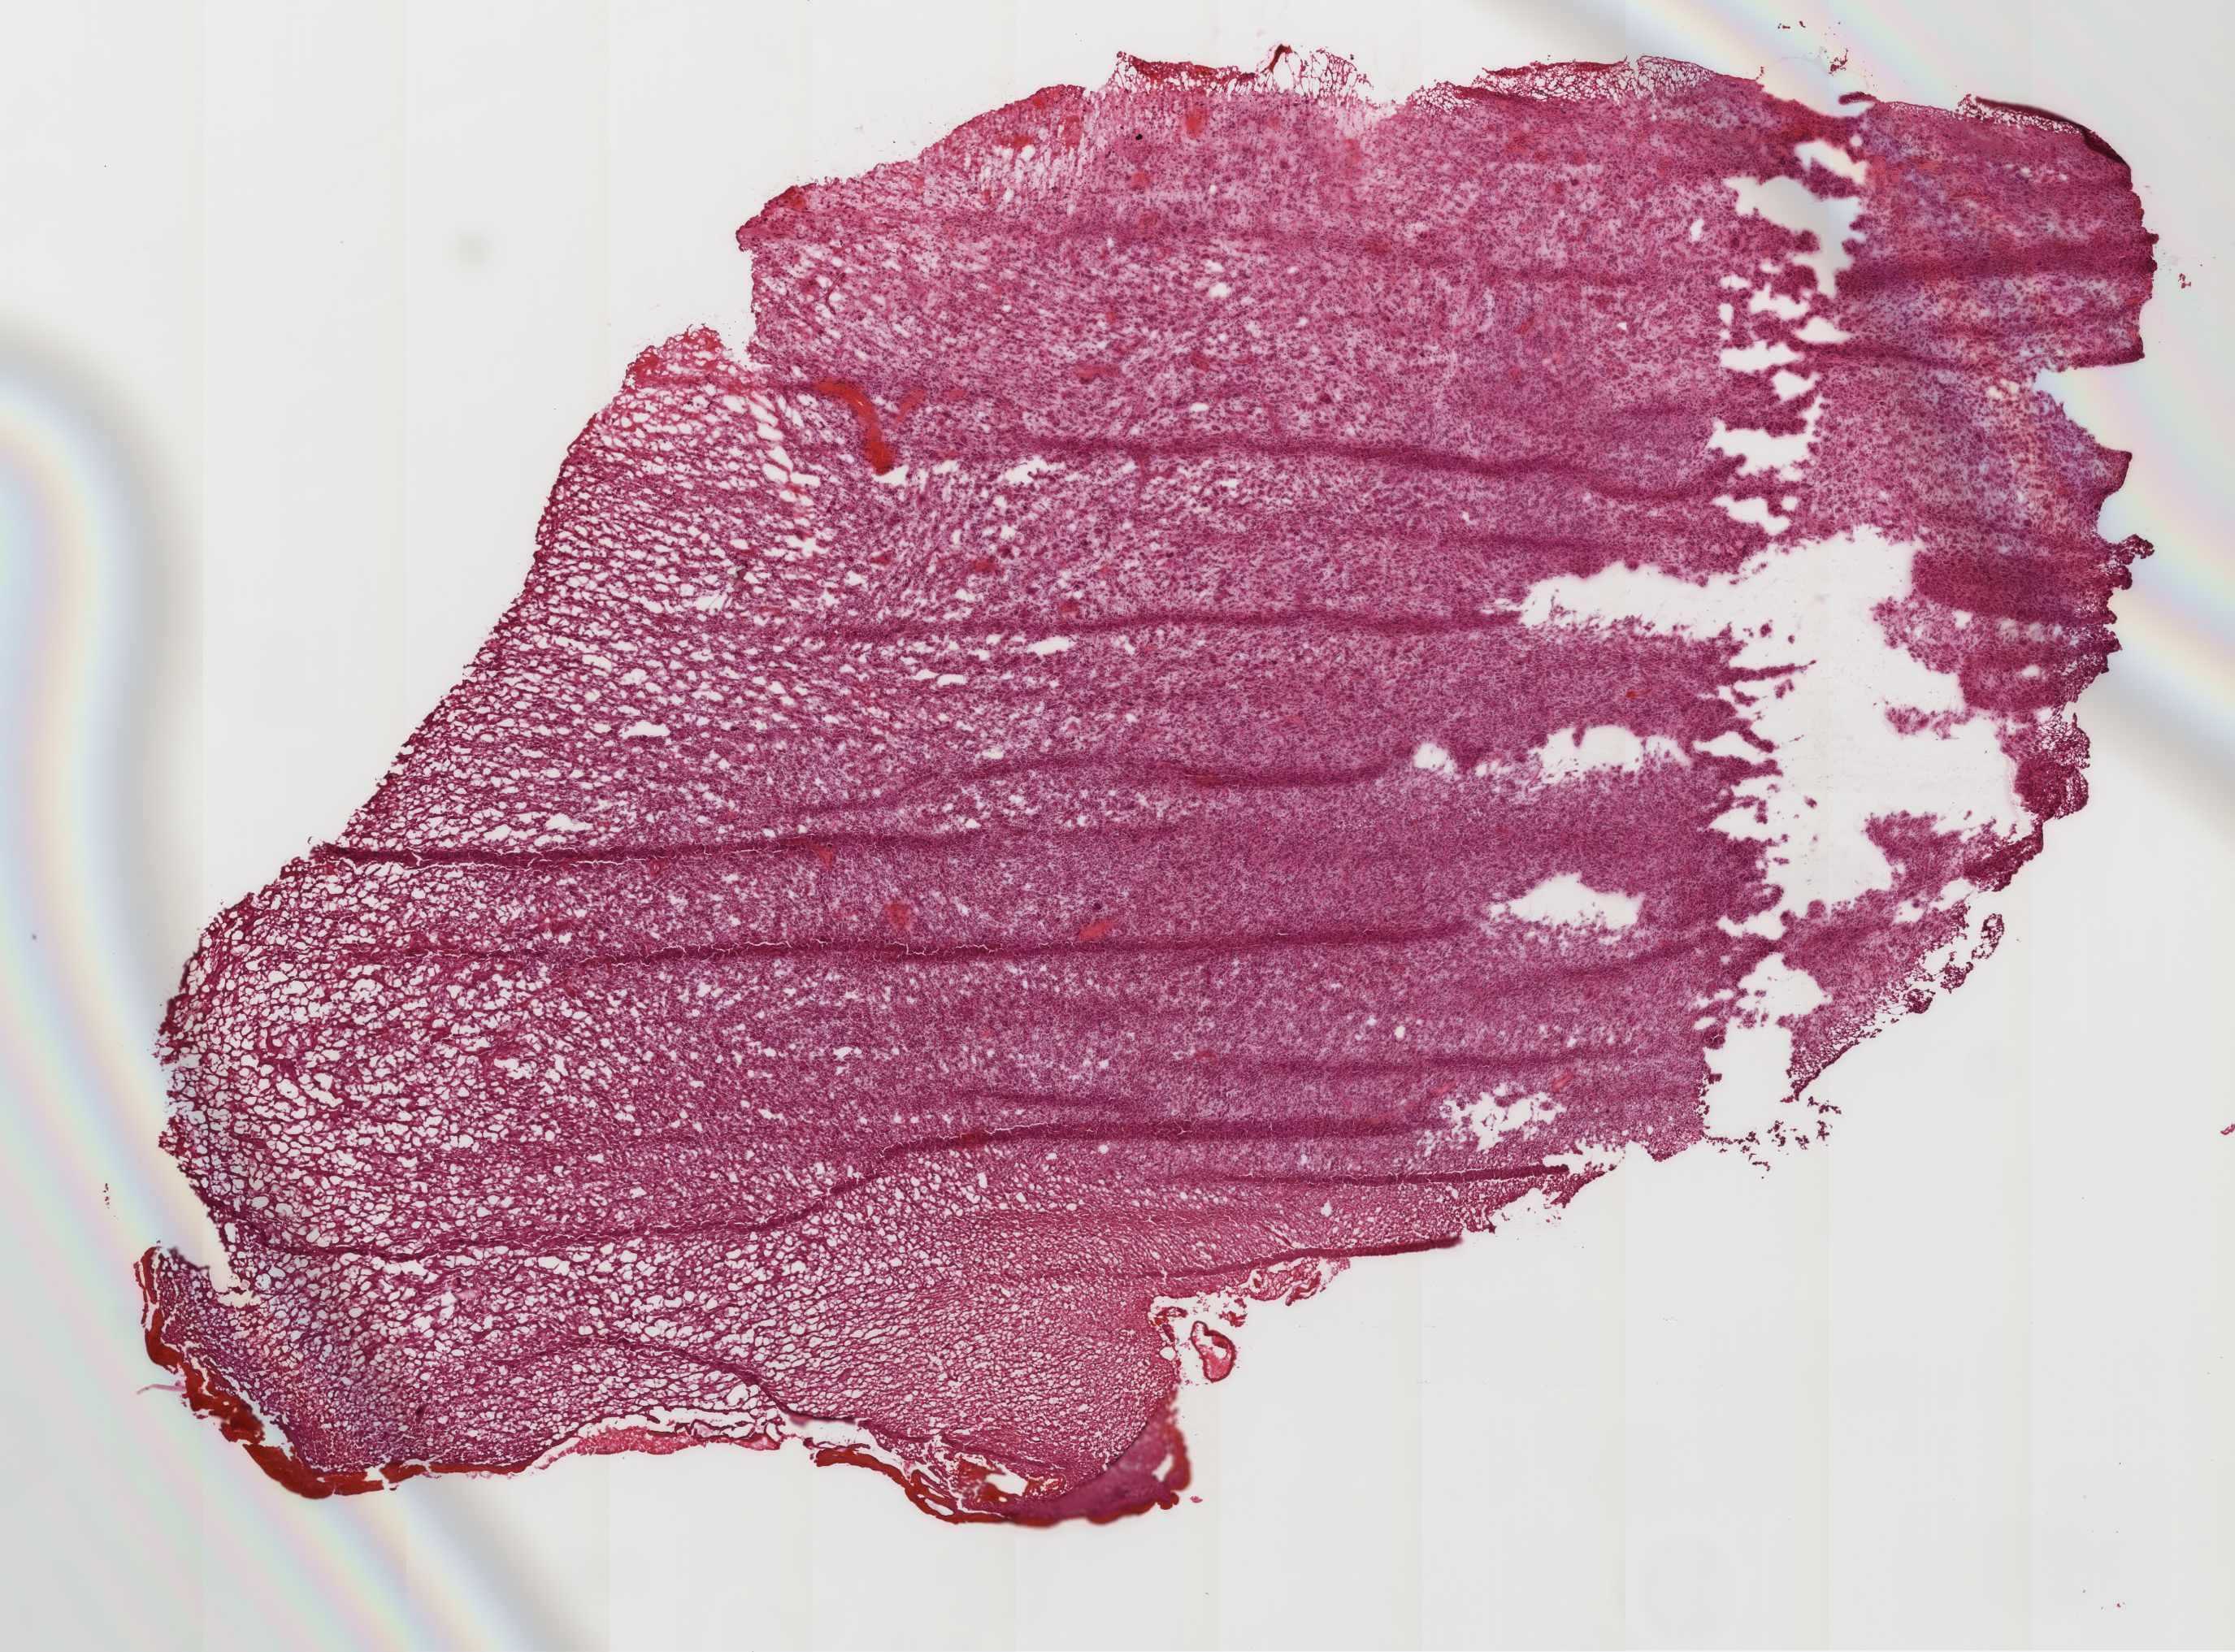
Whole-slide histology image, H&E-stained — a low-resolution overview of the entire scanned area, about 11.0 x 8.2 mm (slide scanned at 20x); frozen section from the top of the tissue portion; sample: primary tumour, brain. Female patient; age at initial diagnosis 59 years. Composition of this section per pathologist review: tumour cells 100%, tumour nuclei 85%, normal cells 0%, stromal cells 0%, necrosis 0%.
Pathologic diagnosis: Glioblastoma.